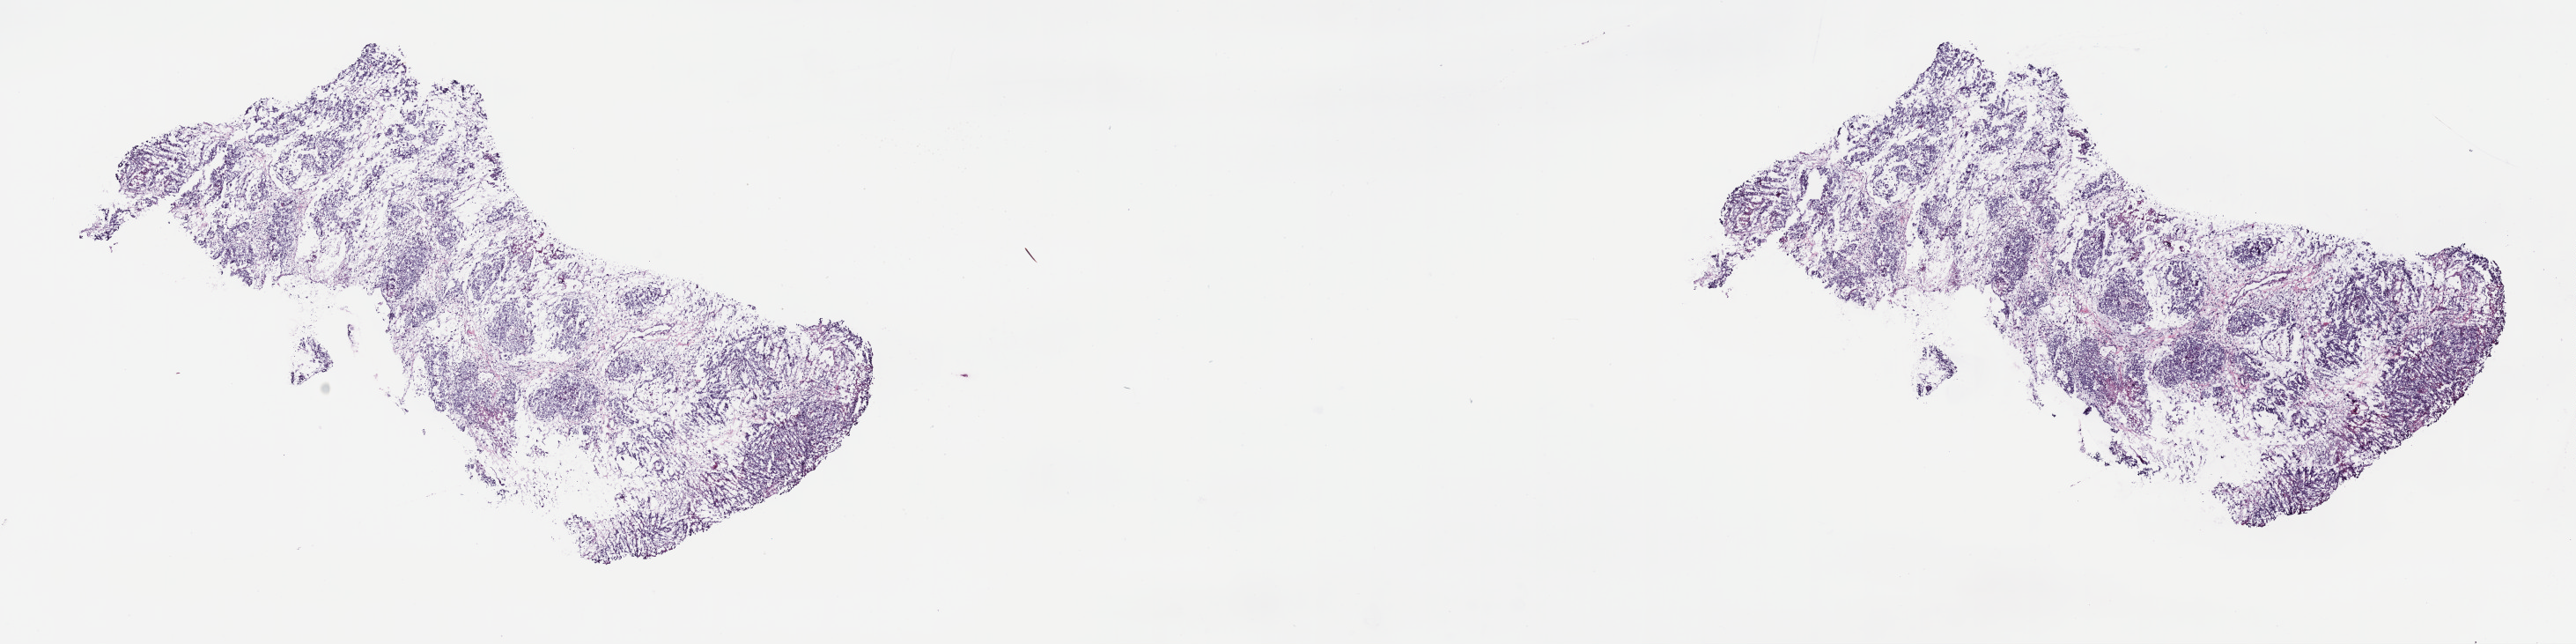
H&E whole-slide image, a low-resolution overview of the entire scanned area, about 23.7 x 5.9 mm (slide scanned at 40x); frozen section from the top of the tissue portion; testis, primary tumour sample. Male, age 41 years at initial diagnosis. Slide review estimates, as recorded: tumour cells 85%, tumour nuclei 65%, normal cells 0%, stromal cells 0%, necrosis 15%. Infiltration values recorded for this section: lymphocyte infiltration 0%, monocyte infiltration 0%, neutrophil infiltration 0%.
Laterality: left. AJCC pathologic stage: IB. Histologic diagnosis: Embryonal carcinoma, NOS.